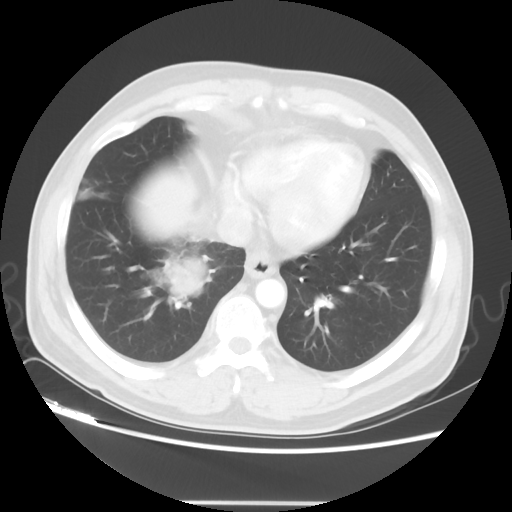
Chest CT, one axial slice. Slice 13 of 48 in the series (ordered by position). 120 kVp. Lung window (W 1500 / L -600 HU). 512 × 512 image matrix, field of view 390 × 390 mm. Patient: male, 53 years. Case-level facts recorded for this patient, not image findings: clinical TNM (as recorded): T2 N3 M0.
Structures marked on this image (bounding box drawn by a radiologist):
- lung tumour (recorded histology: small cell carcinoma): bounding box <157,251,209,306> (left, top, right, bottom; pixels)